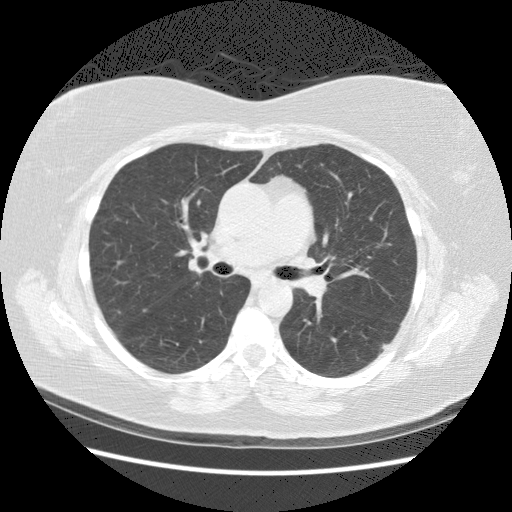
Axial slice from a low-dose chest CT screening exam. Second screening round (one year after baseline). Lung window (W 1500 / L -600 HU). 2.5 mm slice thickness. 120 kVp. 512 × 512 image matrix, field of view 360 × 360 mm. Female, age 57 years at enrolment. Current smoker at enrolment.
Expert-annotated lung lesion, bounding box (x1, y1, x2, y2) in pixels: (356, 327, 402, 372). Reader record for this screening exam (exam-level; its link to the box is not recorded): non-calcified nodule or mass ≥4 mm, left lower lobe, 19 × 9 mm, poorly defined margins, mixed attenuation, pre-existing on the prior screen: yes; interval growth: yes. Official screen result: positive, other. Lung cancer was diagnosed 560 days after this screen (after the third annual screen): squamous cell carcinoma, NOS, left lower lobe, poorly differentiated (G3), stage IB (AJCC 6th edition), 40 mm at pathology.